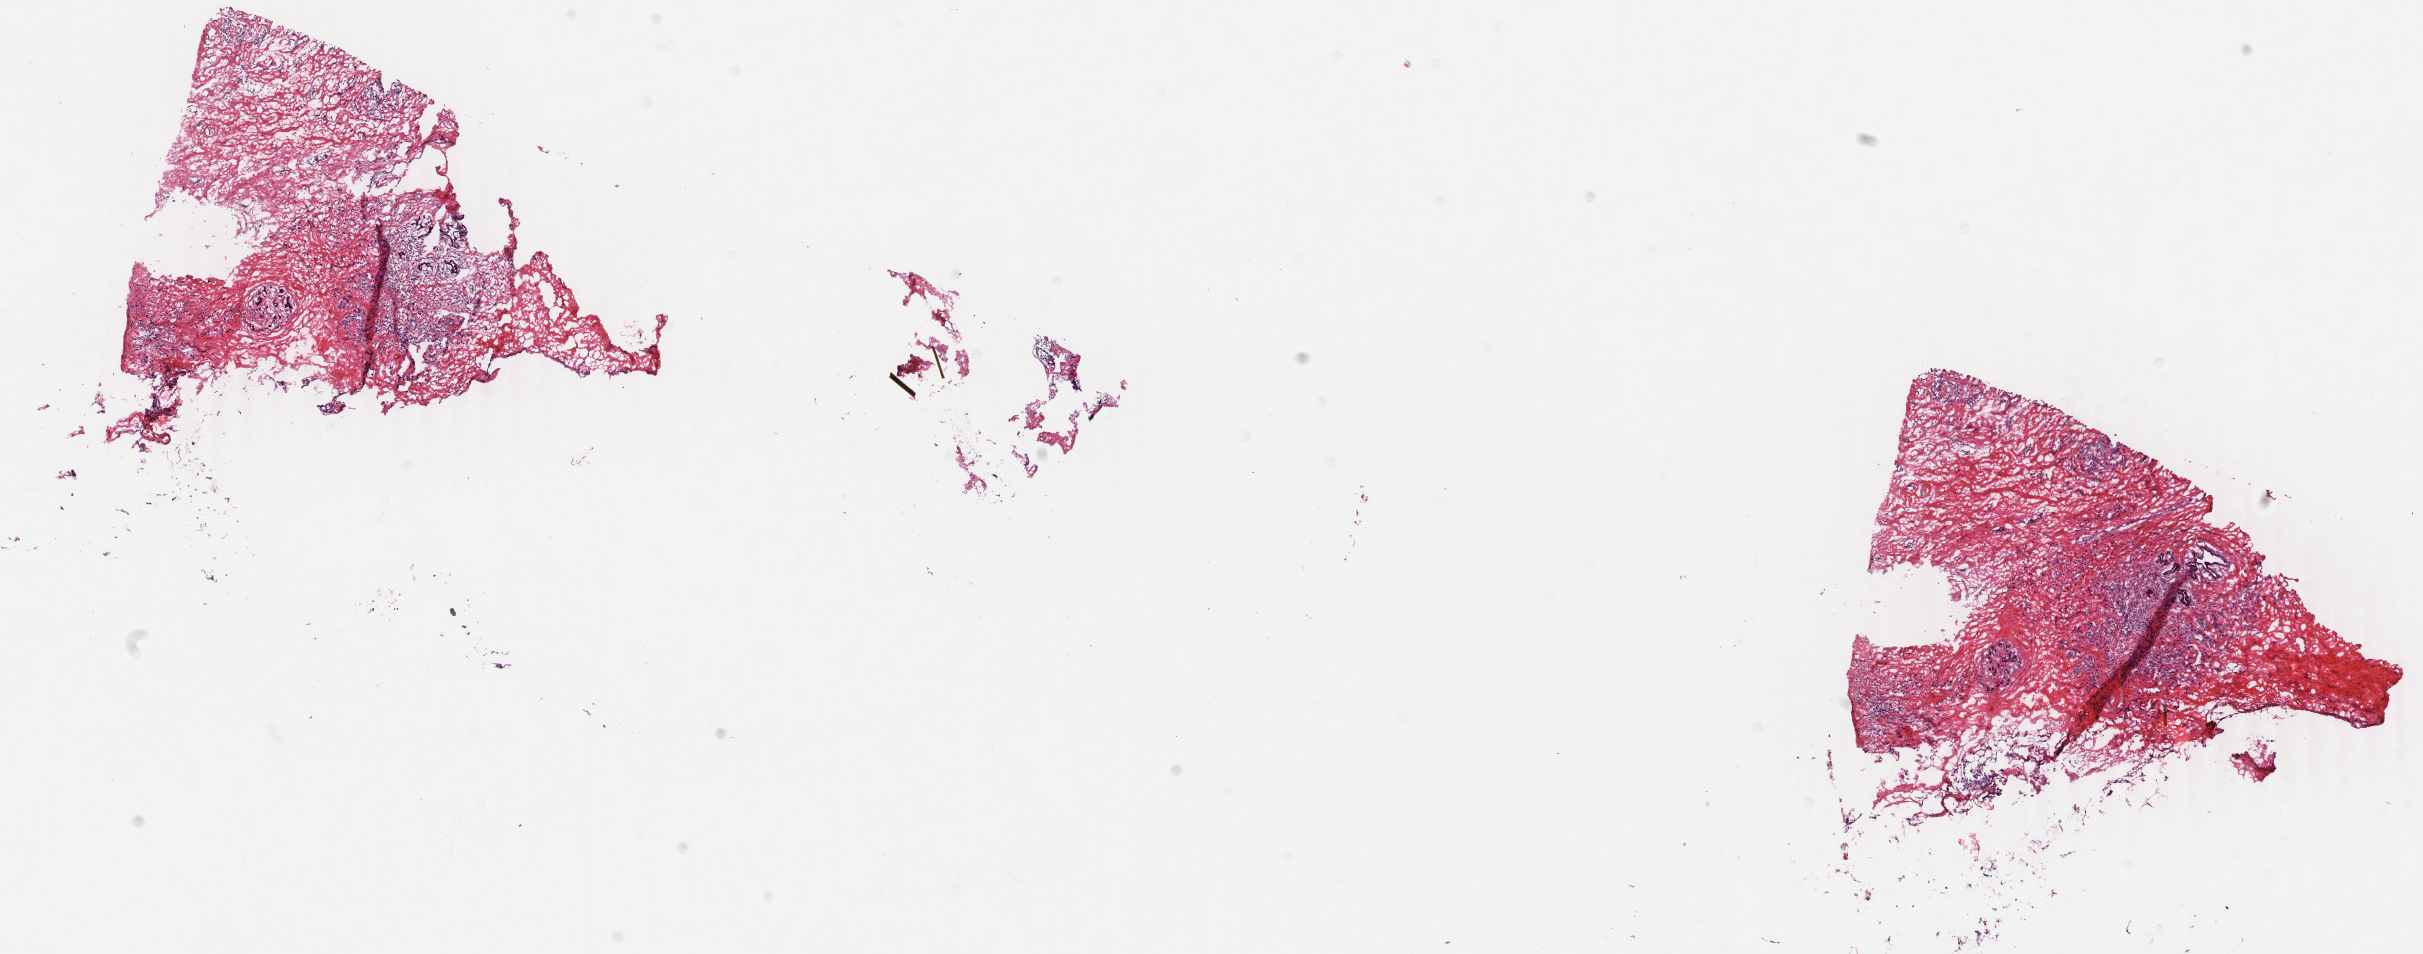
Digitized H&E tissue section (whole slide) — a low-resolution overview of the entire scanned area, about 19.3 x 7.6 mm (acquisition: 40x scan), frozen section, sample: primary tumour, breast. Female patient; age at initial diagnosis 48 years. Composition of this section per pathologist review: tumour cells 50%, tumour nuclei 60%.
Histologic diagnosis: Lobular carcinoma, NOS.